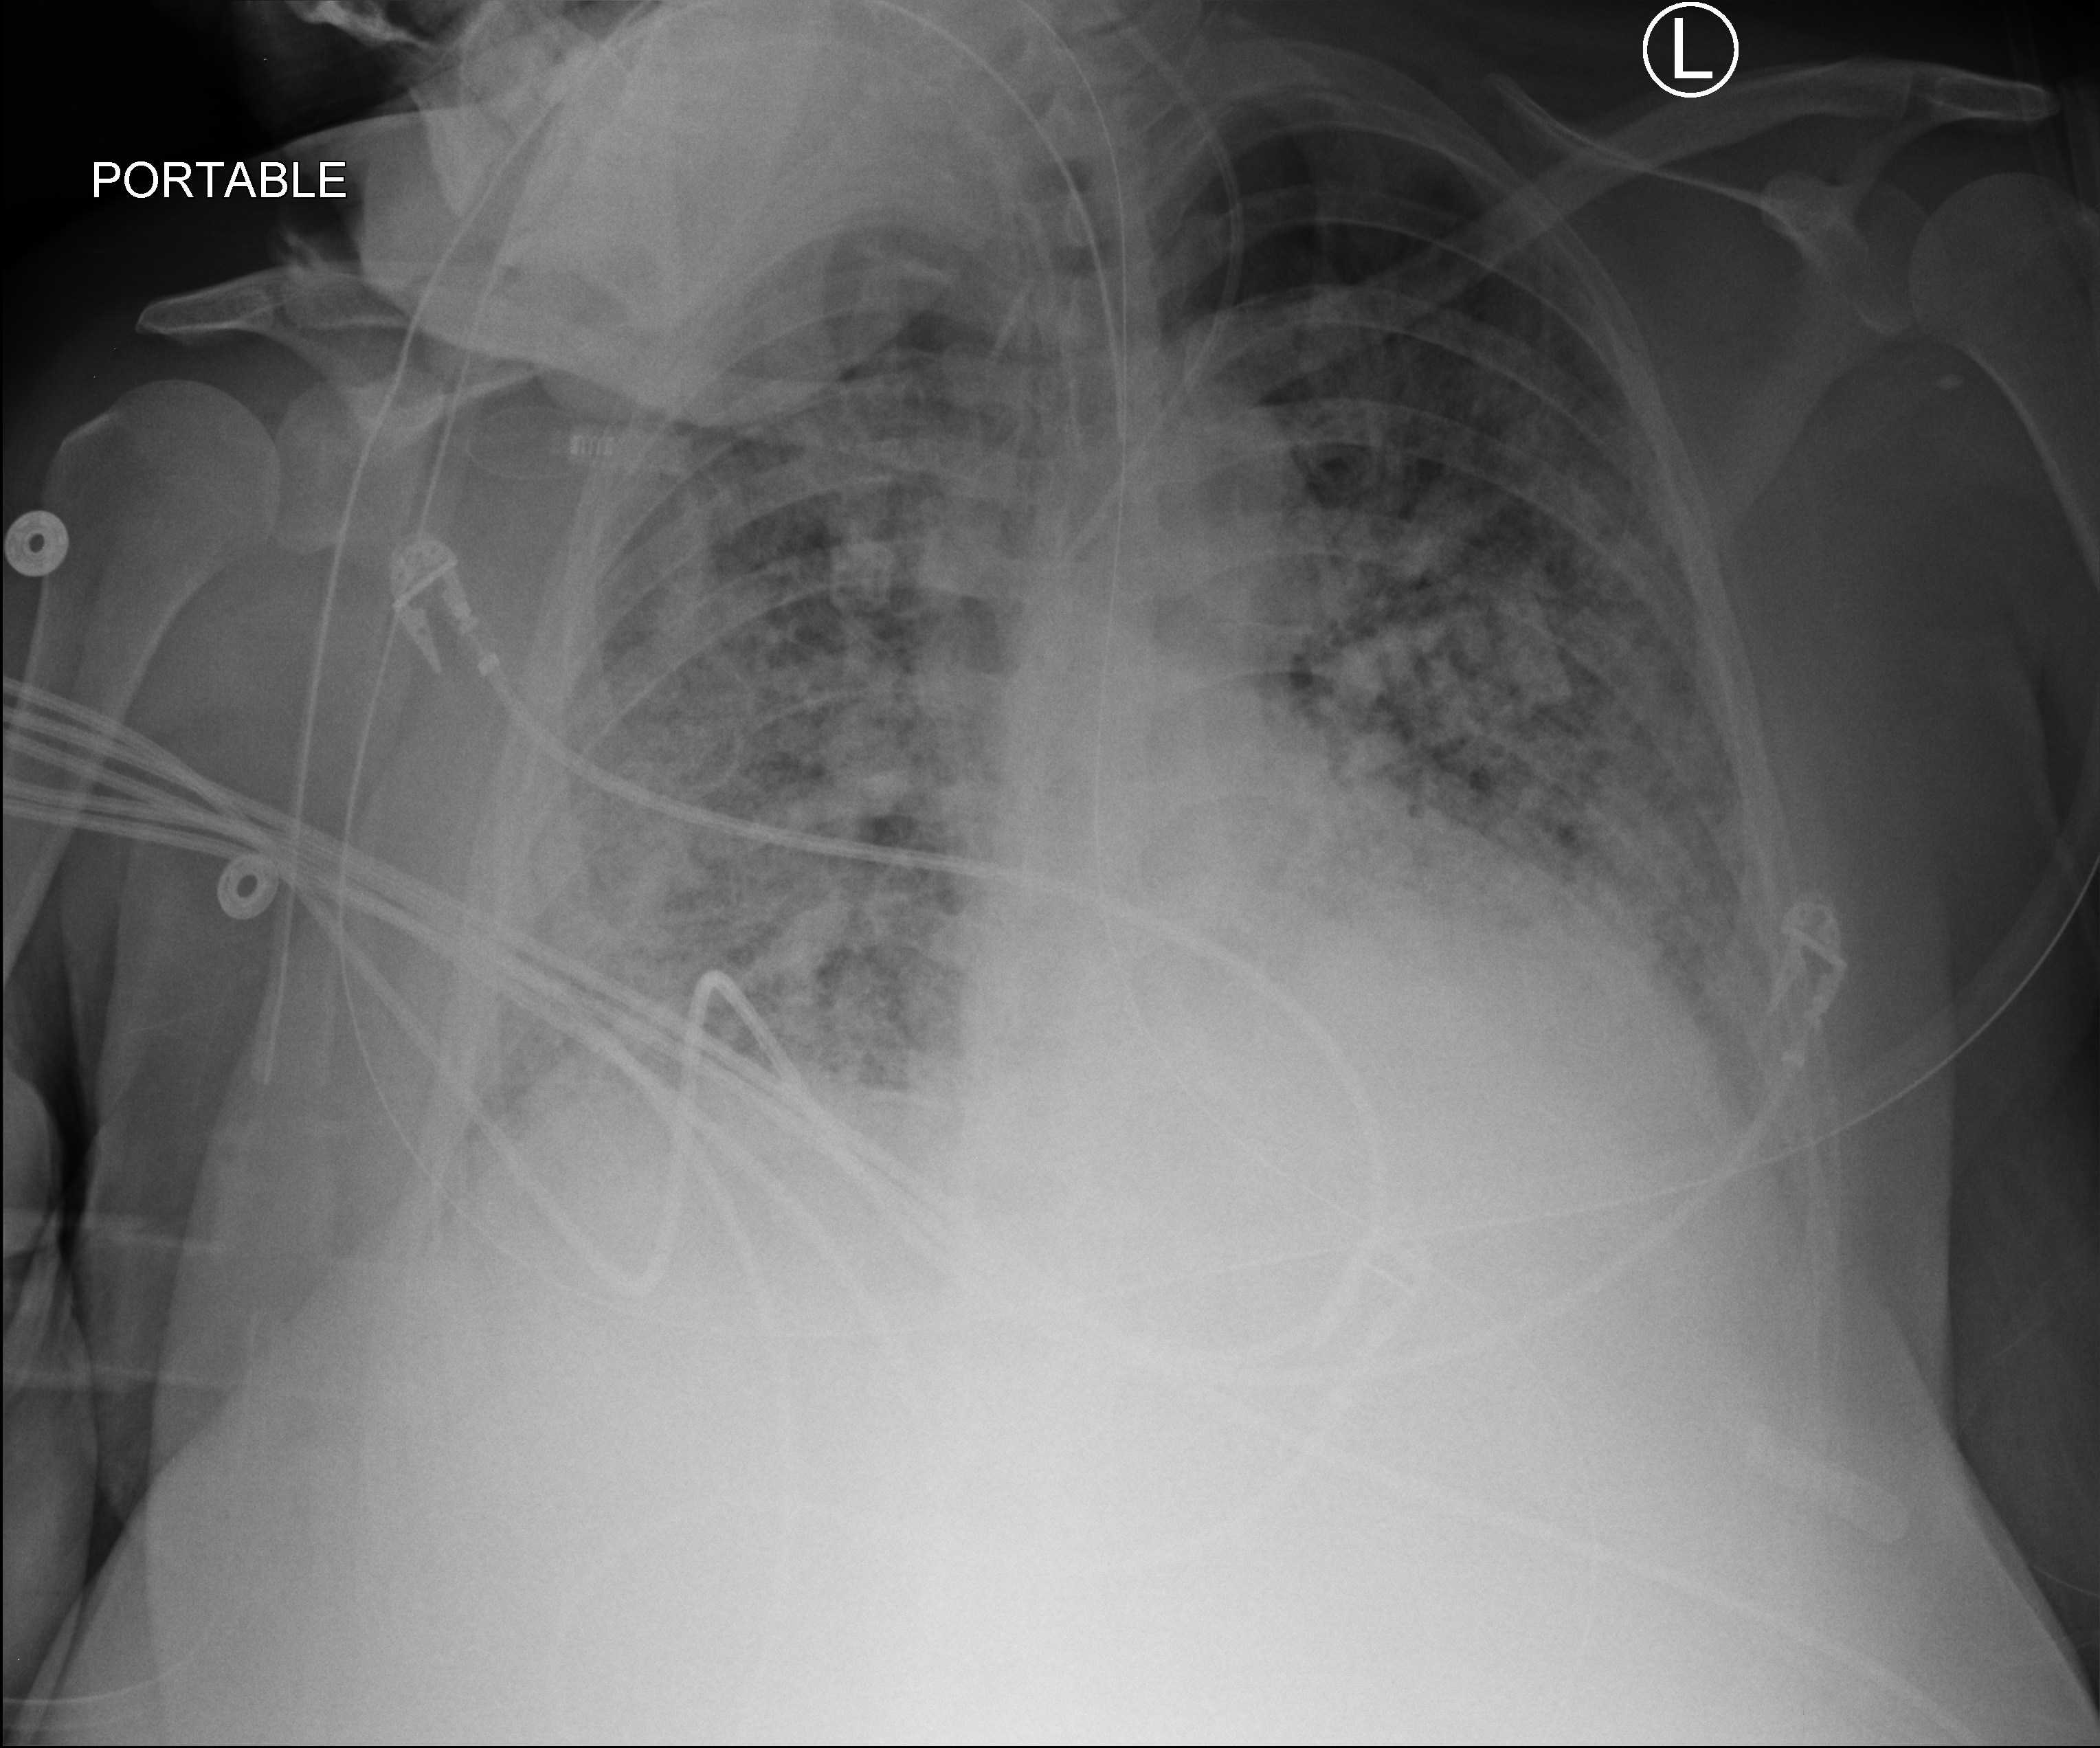
Portable chest radiograph, anteroposterior (AP) projection. Patient hospitalised with COVID-19; female, aged 18–59 years.
Hospital-stay facts (about this admission, not read from this image; timing relative to this image not recorded):
- mechanically ventilated during this hospital stay: yes
- length of hospital stay: 33 days
- admitted to intensive care during this hospital stay: no